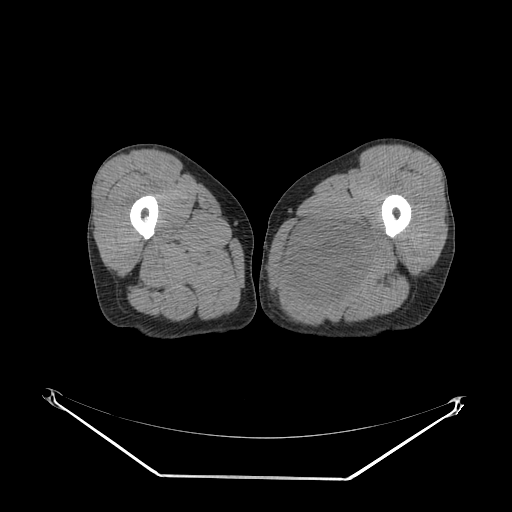
CT of an extremity soft-tissue mass (from a PET/CT study), one axial slice. Position 23 of 267 along the scan axis. Soft-tissue window (W 400 / L 40 HU). 3.75 mm slice thickness. 512 × 512 image matrix, field of view 500 × 500 mm. Male patient. Case-level facts recorded for this patient, not image findings: histological type: pleiomorphic liposarcoma; grade: high; site of the primary tumour: left thigh.
Outlined on this slice (expert contour drawn on MRI and transferred to this co-registered scan by the dataset authors):
- gross tumour volume including surrounding oedema: box from (x=288, y=214) to (x=387, y=307) px
- gross tumour volume (mass): (x=292, y=219)–(x=369, y=302)